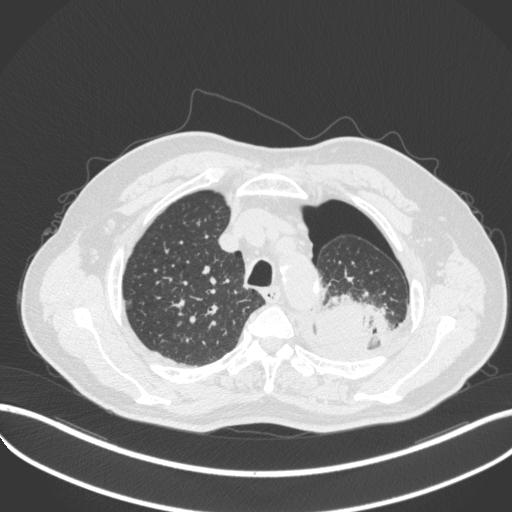
Chest CT, one axial slice; slice 402 of 466 in the series (ordered by position); 120 kVp; lung window (W 1500 / L -600 HU); 1 mm slice thickness; 512 × 512 image matrix, field of view 400 × 400 mm. Male patient, age 76 years. From the clinical record (not read from this slice): clinical TNM (as recorded): T3 N0 M1b.
Annotated regions visible in this slice (bounding box drawn by a radiologist):
- lung tumour (recorded histology: adenocarcinoma): bounding box (x1, y1, x2, y2) in pixels: (315, 293, 389, 354)